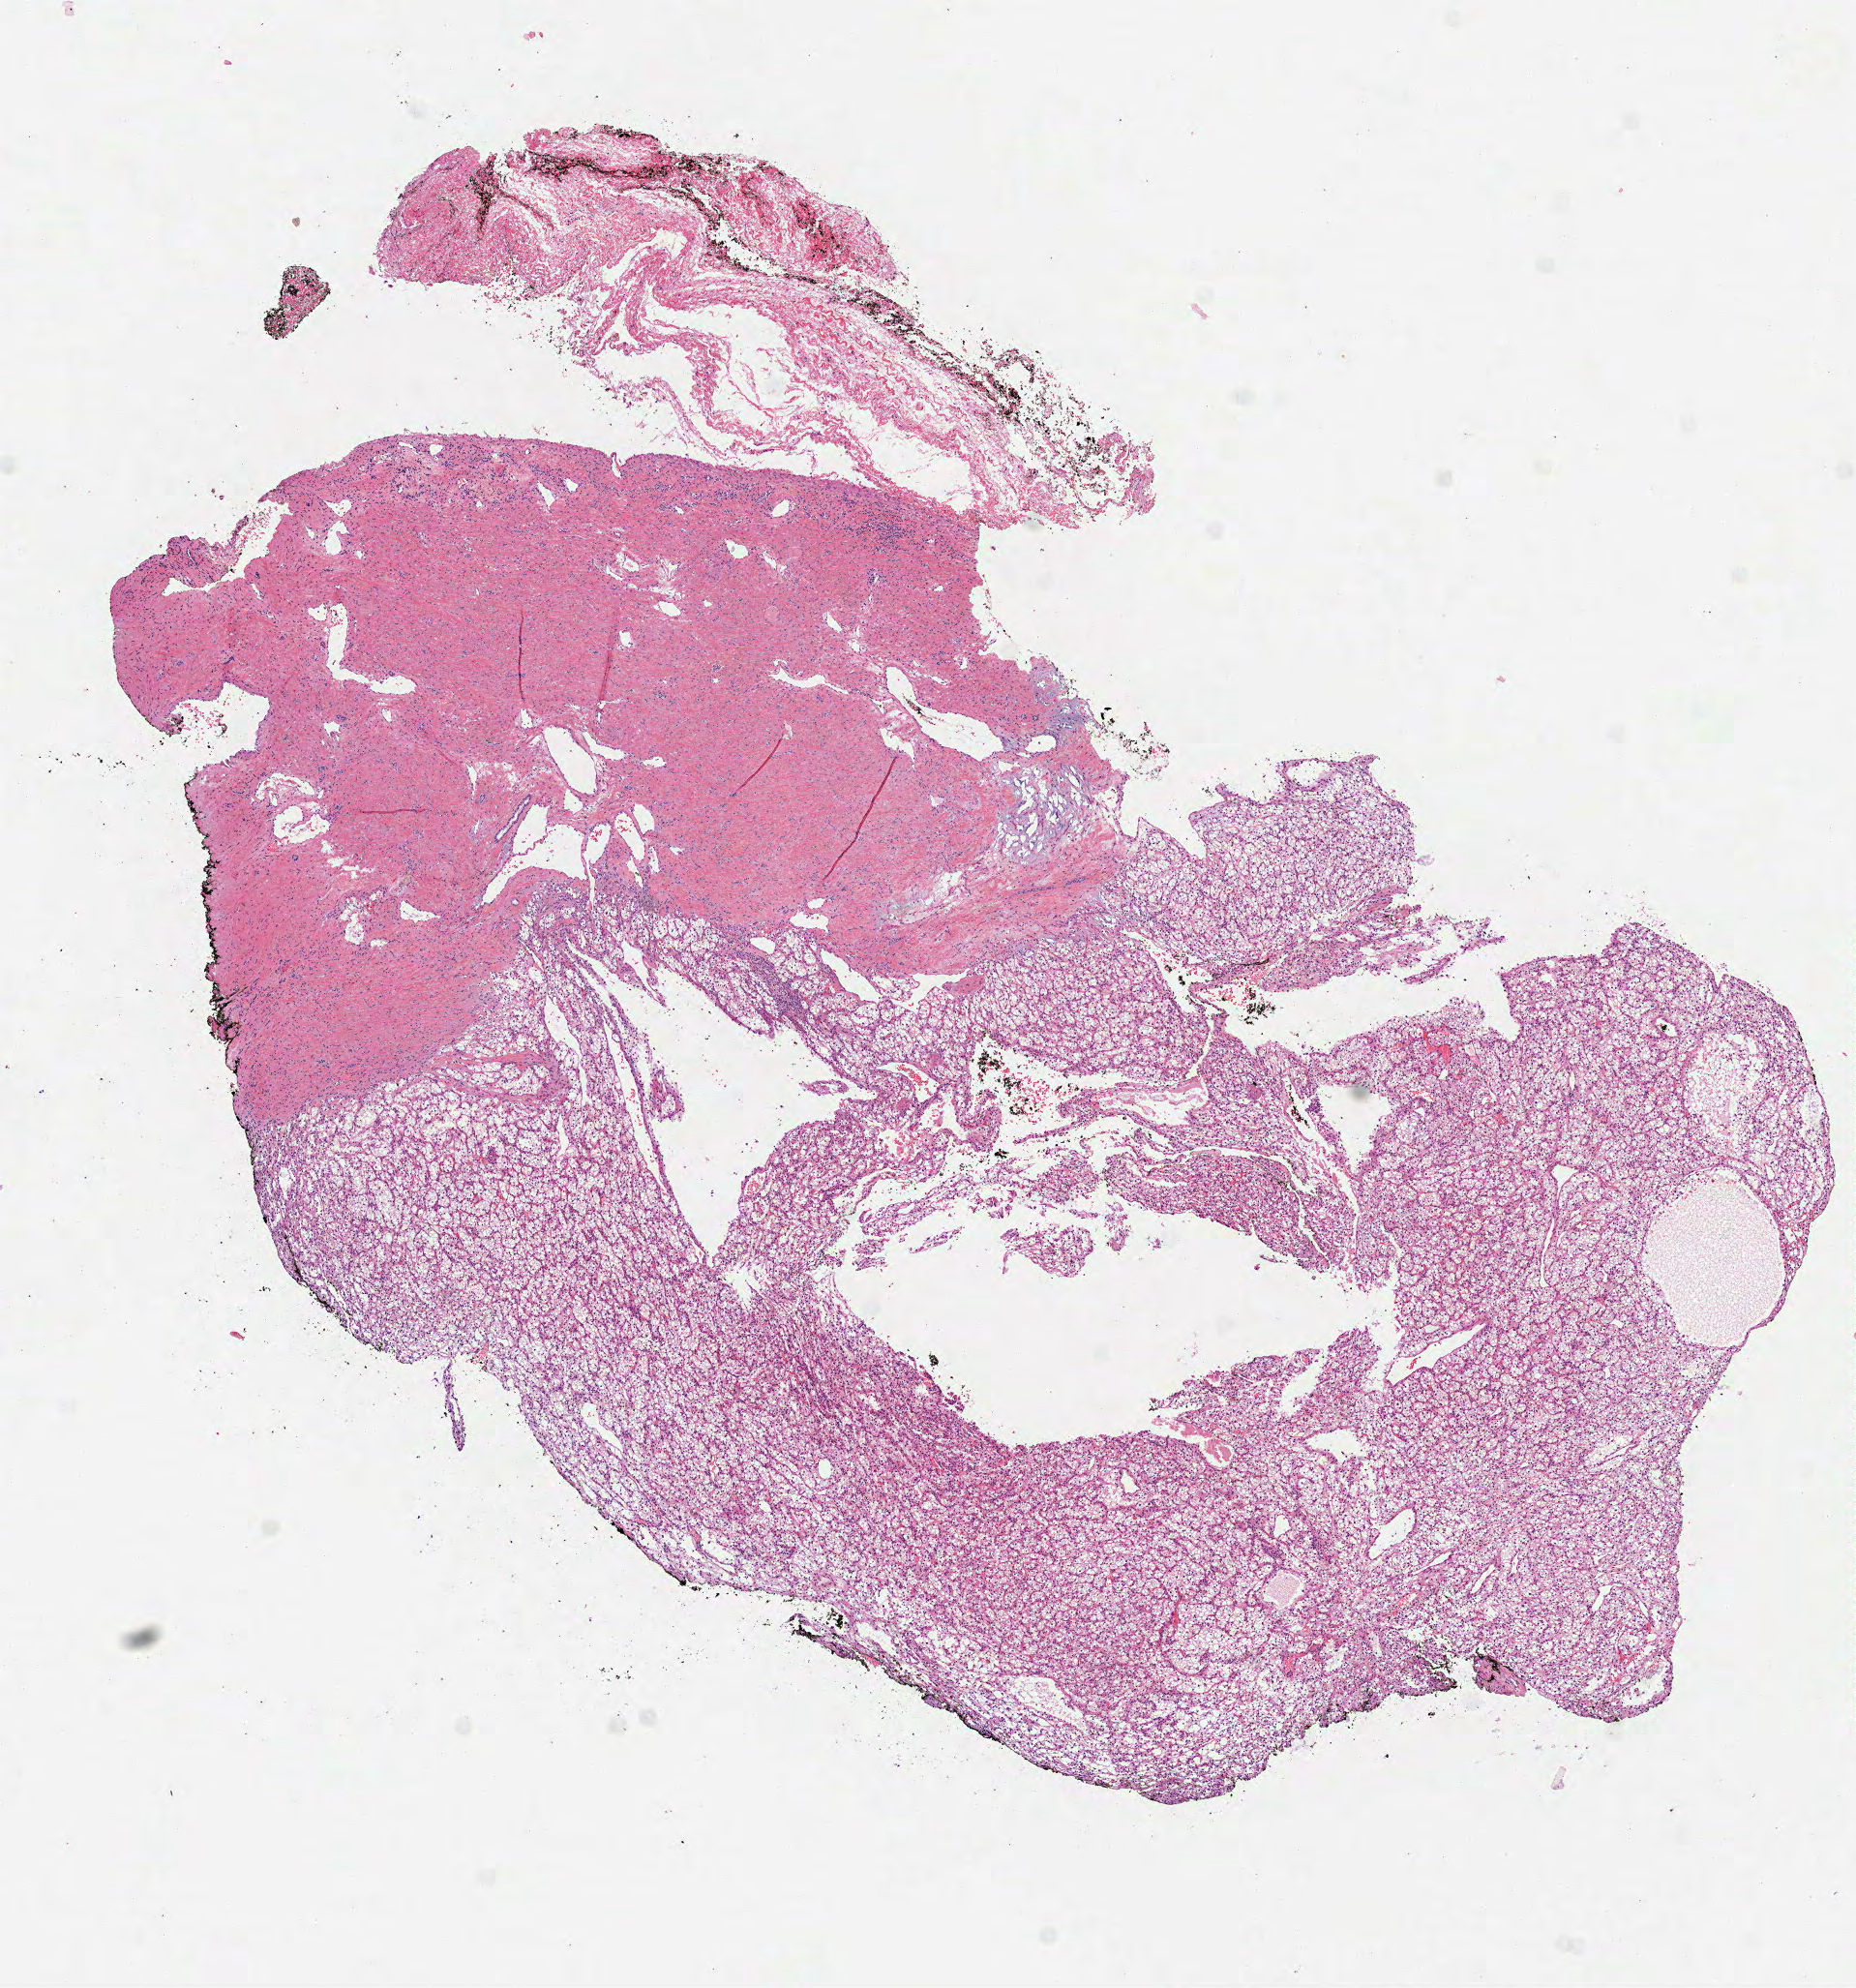
Digitized H&E tissue section (whole slide), shown as a low-resolution overview of the whole scanned area (about 7.7 x 8.3 mm, from a 40x scan), FFPE section, sample: primary tumour, kidney. Female, age 48 years at initial diagnosis. Histologic grade: G2 (moderately differentiated).
TNM: T1b N0 M0. AJCC pathologic stage: I. Histologic diagnosis: Clear cell adenocarcinoma, NOS.